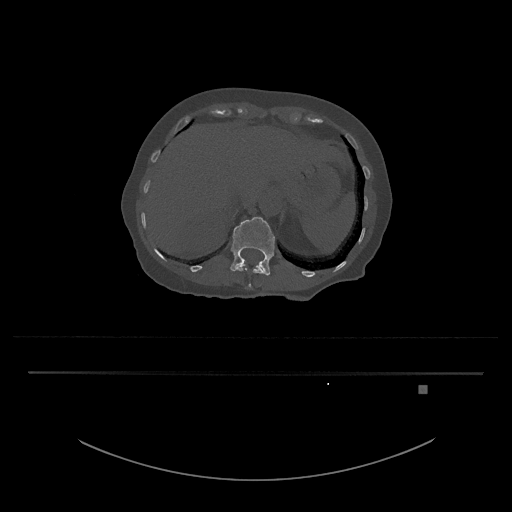
CT including the spine, one axial slice. Position 577 of 797 along the scan axis. Bone window (W 1800 / L 400 HU). 512 × 512 image matrix, field of view 500 × 500 mm. Patient: female, 57 years. From the clinical record (not read from this slice): primary cancer: cervical.
Annotated regions visible in this slice (semi-automatically segmented with operator editing):
- L1 vertebra: bounding box [x1, y1, x2, y2] px = [230, 217, 275, 275]
- T12 vertebra: [235, 263, 265, 288]